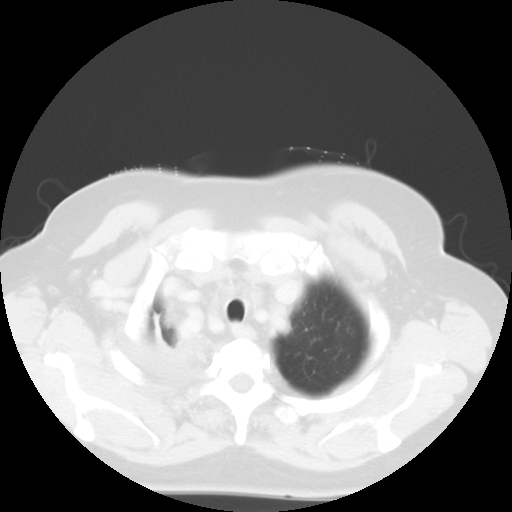
Chest CT, one axial slice. Slice 47 of 52 in the series (ordered by position). Reconstruction kernel STANDARD. Lung window (W 1500 / L -600 HU). 512 × 512 image matrix. Patient: female, 81 years. From the clinical record (not read from this slice): clinical TNM (as recorded): T4 N3 M1b.
Structures marked on this image (bounding box drawn by a radiologist):
- lung tumour (recorded histology: adenocarcinoma): bounding box <151,309,210,377> (left, top, right, bottom; pixels)